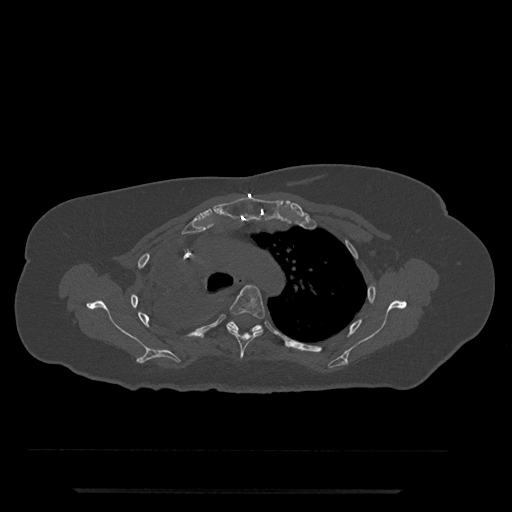
CT including the spine, one axial slice. Position 576 of 797 along the scan axis. 120 kVp. Bone window (W 1800 / L 400 HU). 512 × 512 image matrix, field of view 440 × 440 mm. Female patient, age 51 years. Case-level facts recorded for this patient, not image findings: primary cancer: neuro.
Structures marked on this image (semi-automatic segmentation, software-assisted and operator-edited):
- T4 vertebra: bounding box [x1, y1, x2, y2] px = [212, 285, 265, 359]
- T5 vertebra: [227, 321, 277, 335]